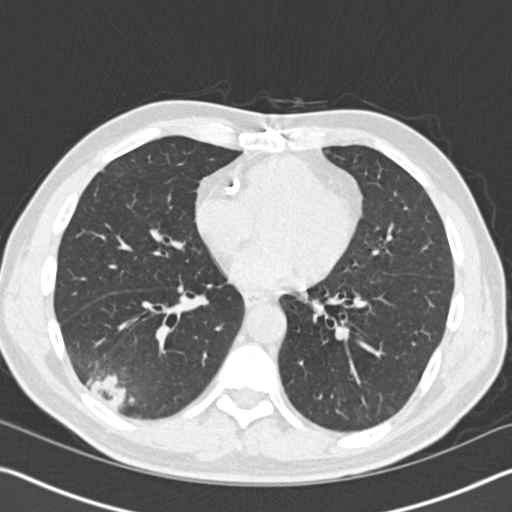
Axial slice from a low-dose chest CT screening exam; baseline screening round; lung window (W 1500 / L -600 HU); 2 mm slice thickness; standard (soft-tissue) reconstruction kernel (B30f); slice 93 of 161 in the series; 512 × 512 image matrix, field of view 340 × 340 mm. Male participant, aged 61 years at enrolment. Current smoker at enrolment.
Expert reader's lesion annotation, bounding box [x1, y1, x2, y2] px = [50, 329, 159, 424]. The exam's reader record, not a measurement of the box and not confirmed to be the same lesion: non-calcified nodule or mass ≥4 mm, right lower lobe, 52 × 36 mm, spiculated (stellate) margins, soft tissue attenuation. Participant outcome: lung cancer diagnosed 392 days after this screen — bronchiolo-alveolar adenocarcinoma, NOS, right lower lobe, moderately differentiated (G2), stage IIIB (AJCC 6th edition), 90 mm at pathology.